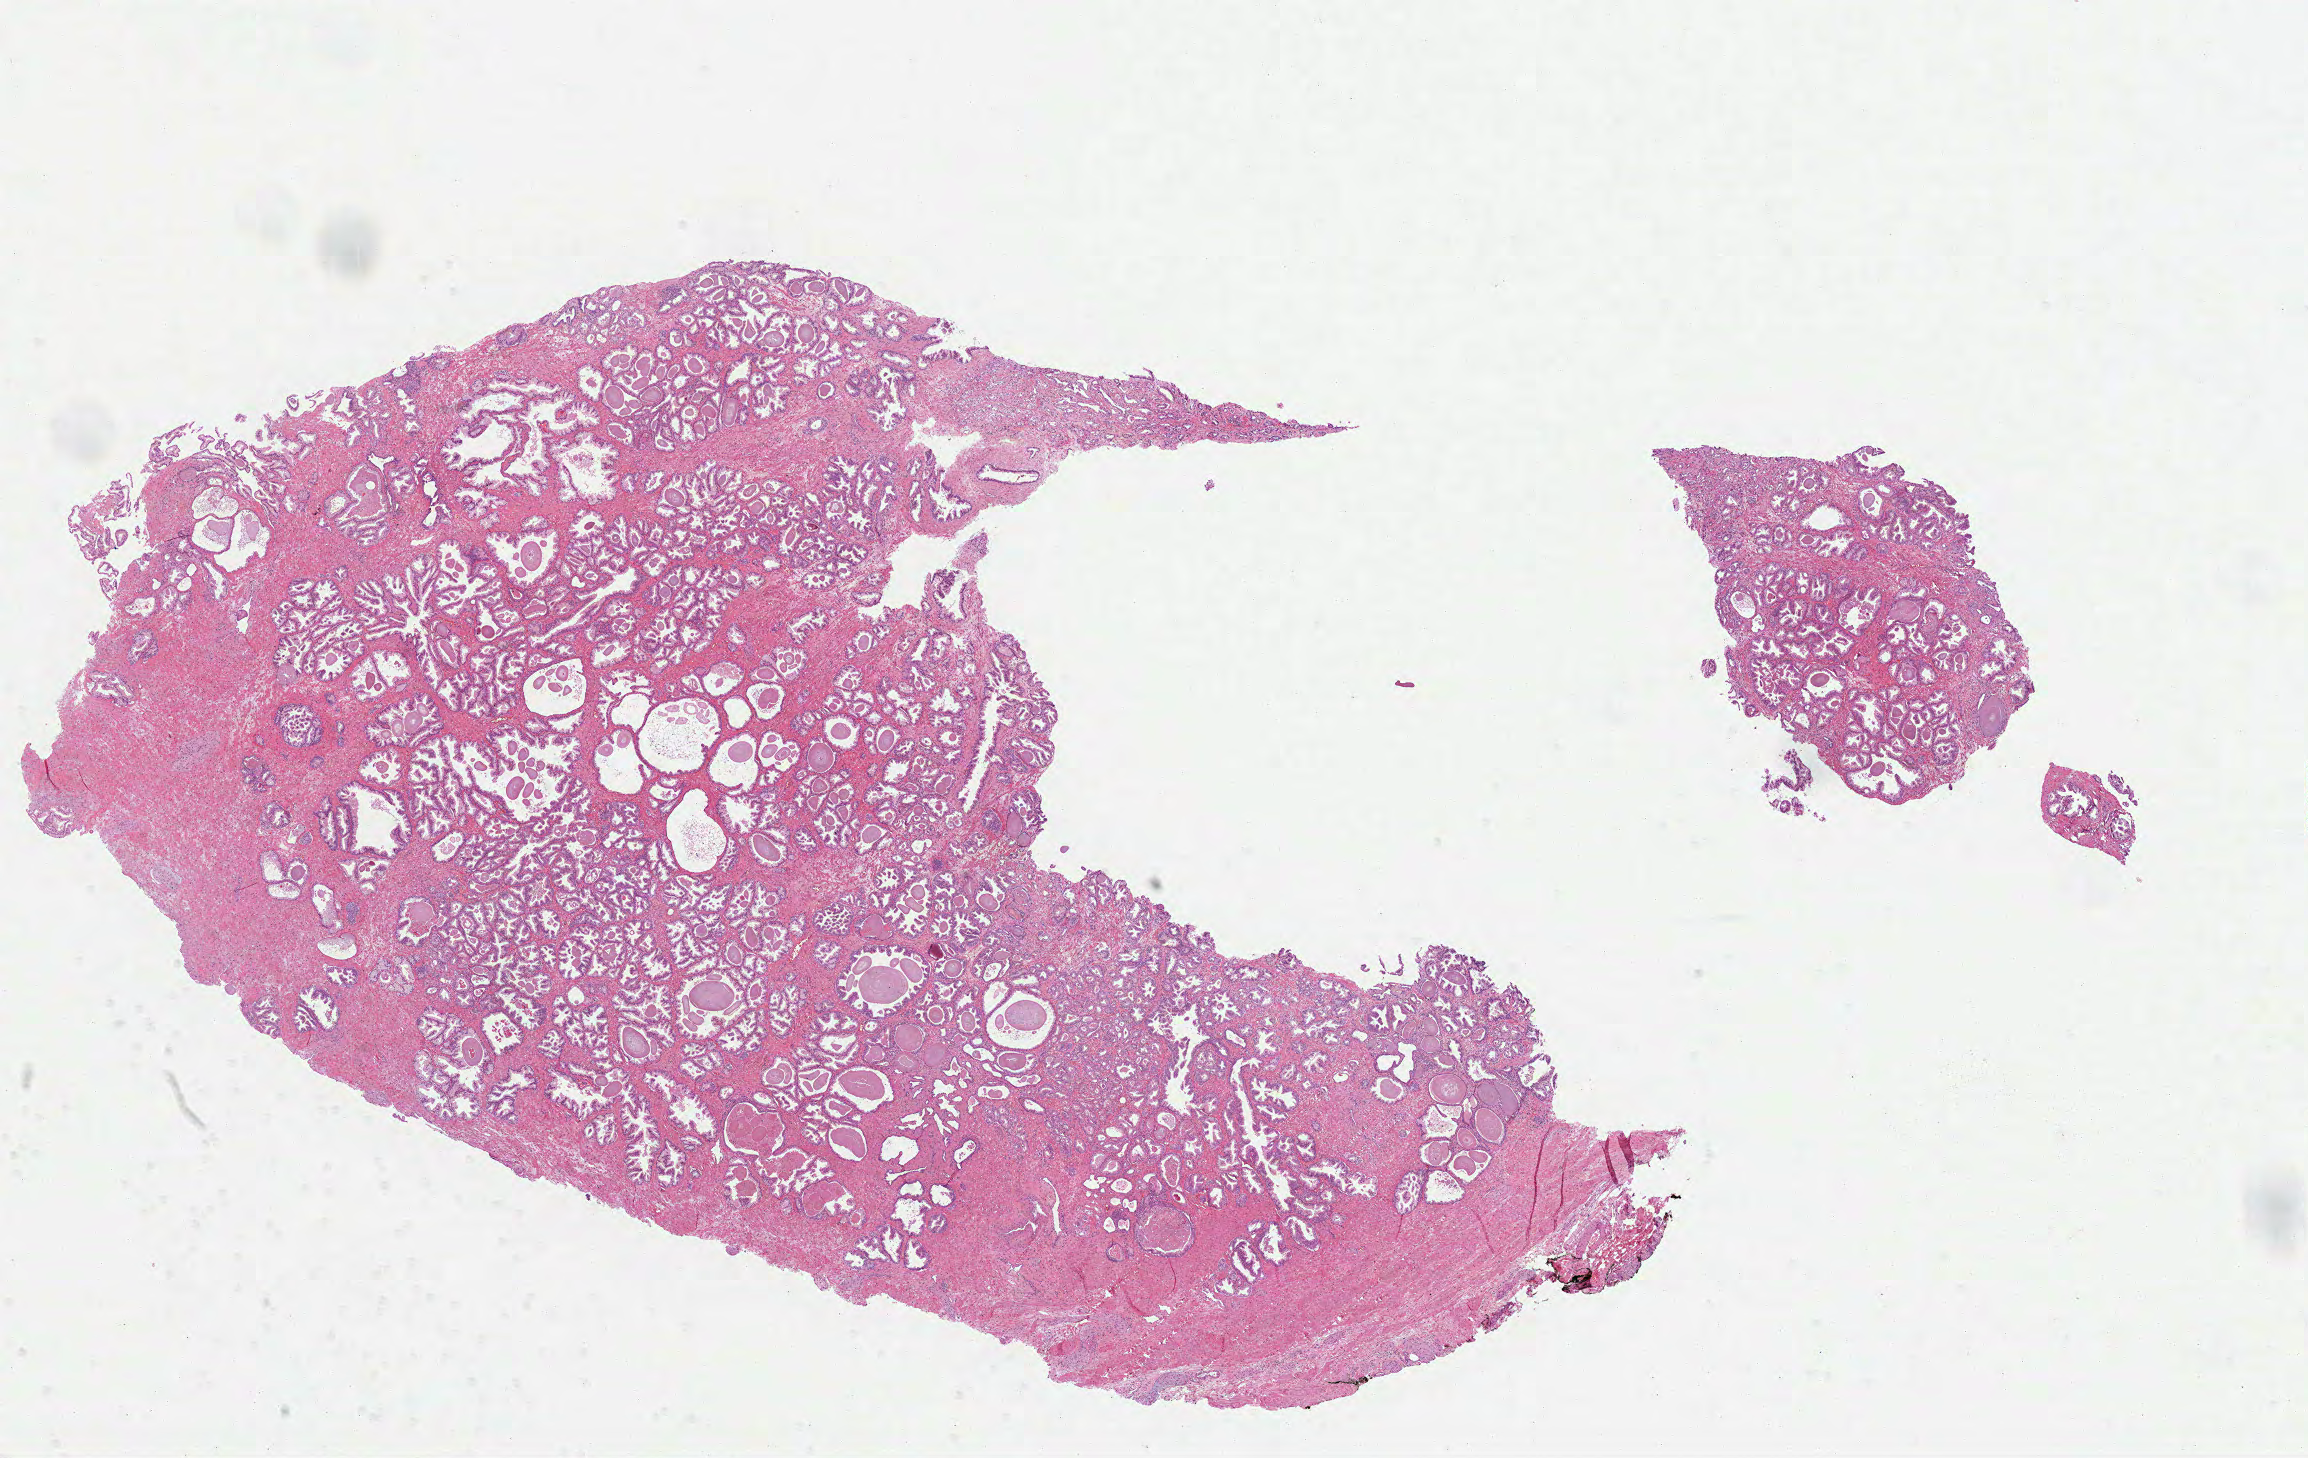
H&E-stained whole-slide image — whole scanned area (about 18.6 x 11.8 mm) shown as a low-resolution overview, formalin-fixed paraffin-embedded (FFPE) diagnostic section, prostate, primary tumour sample. Patient: male, age at initial diagnosis 48 years. Gleason score: 7 (3+4).
- diagnosis: Acinar cell carcinoma (prostate gland)